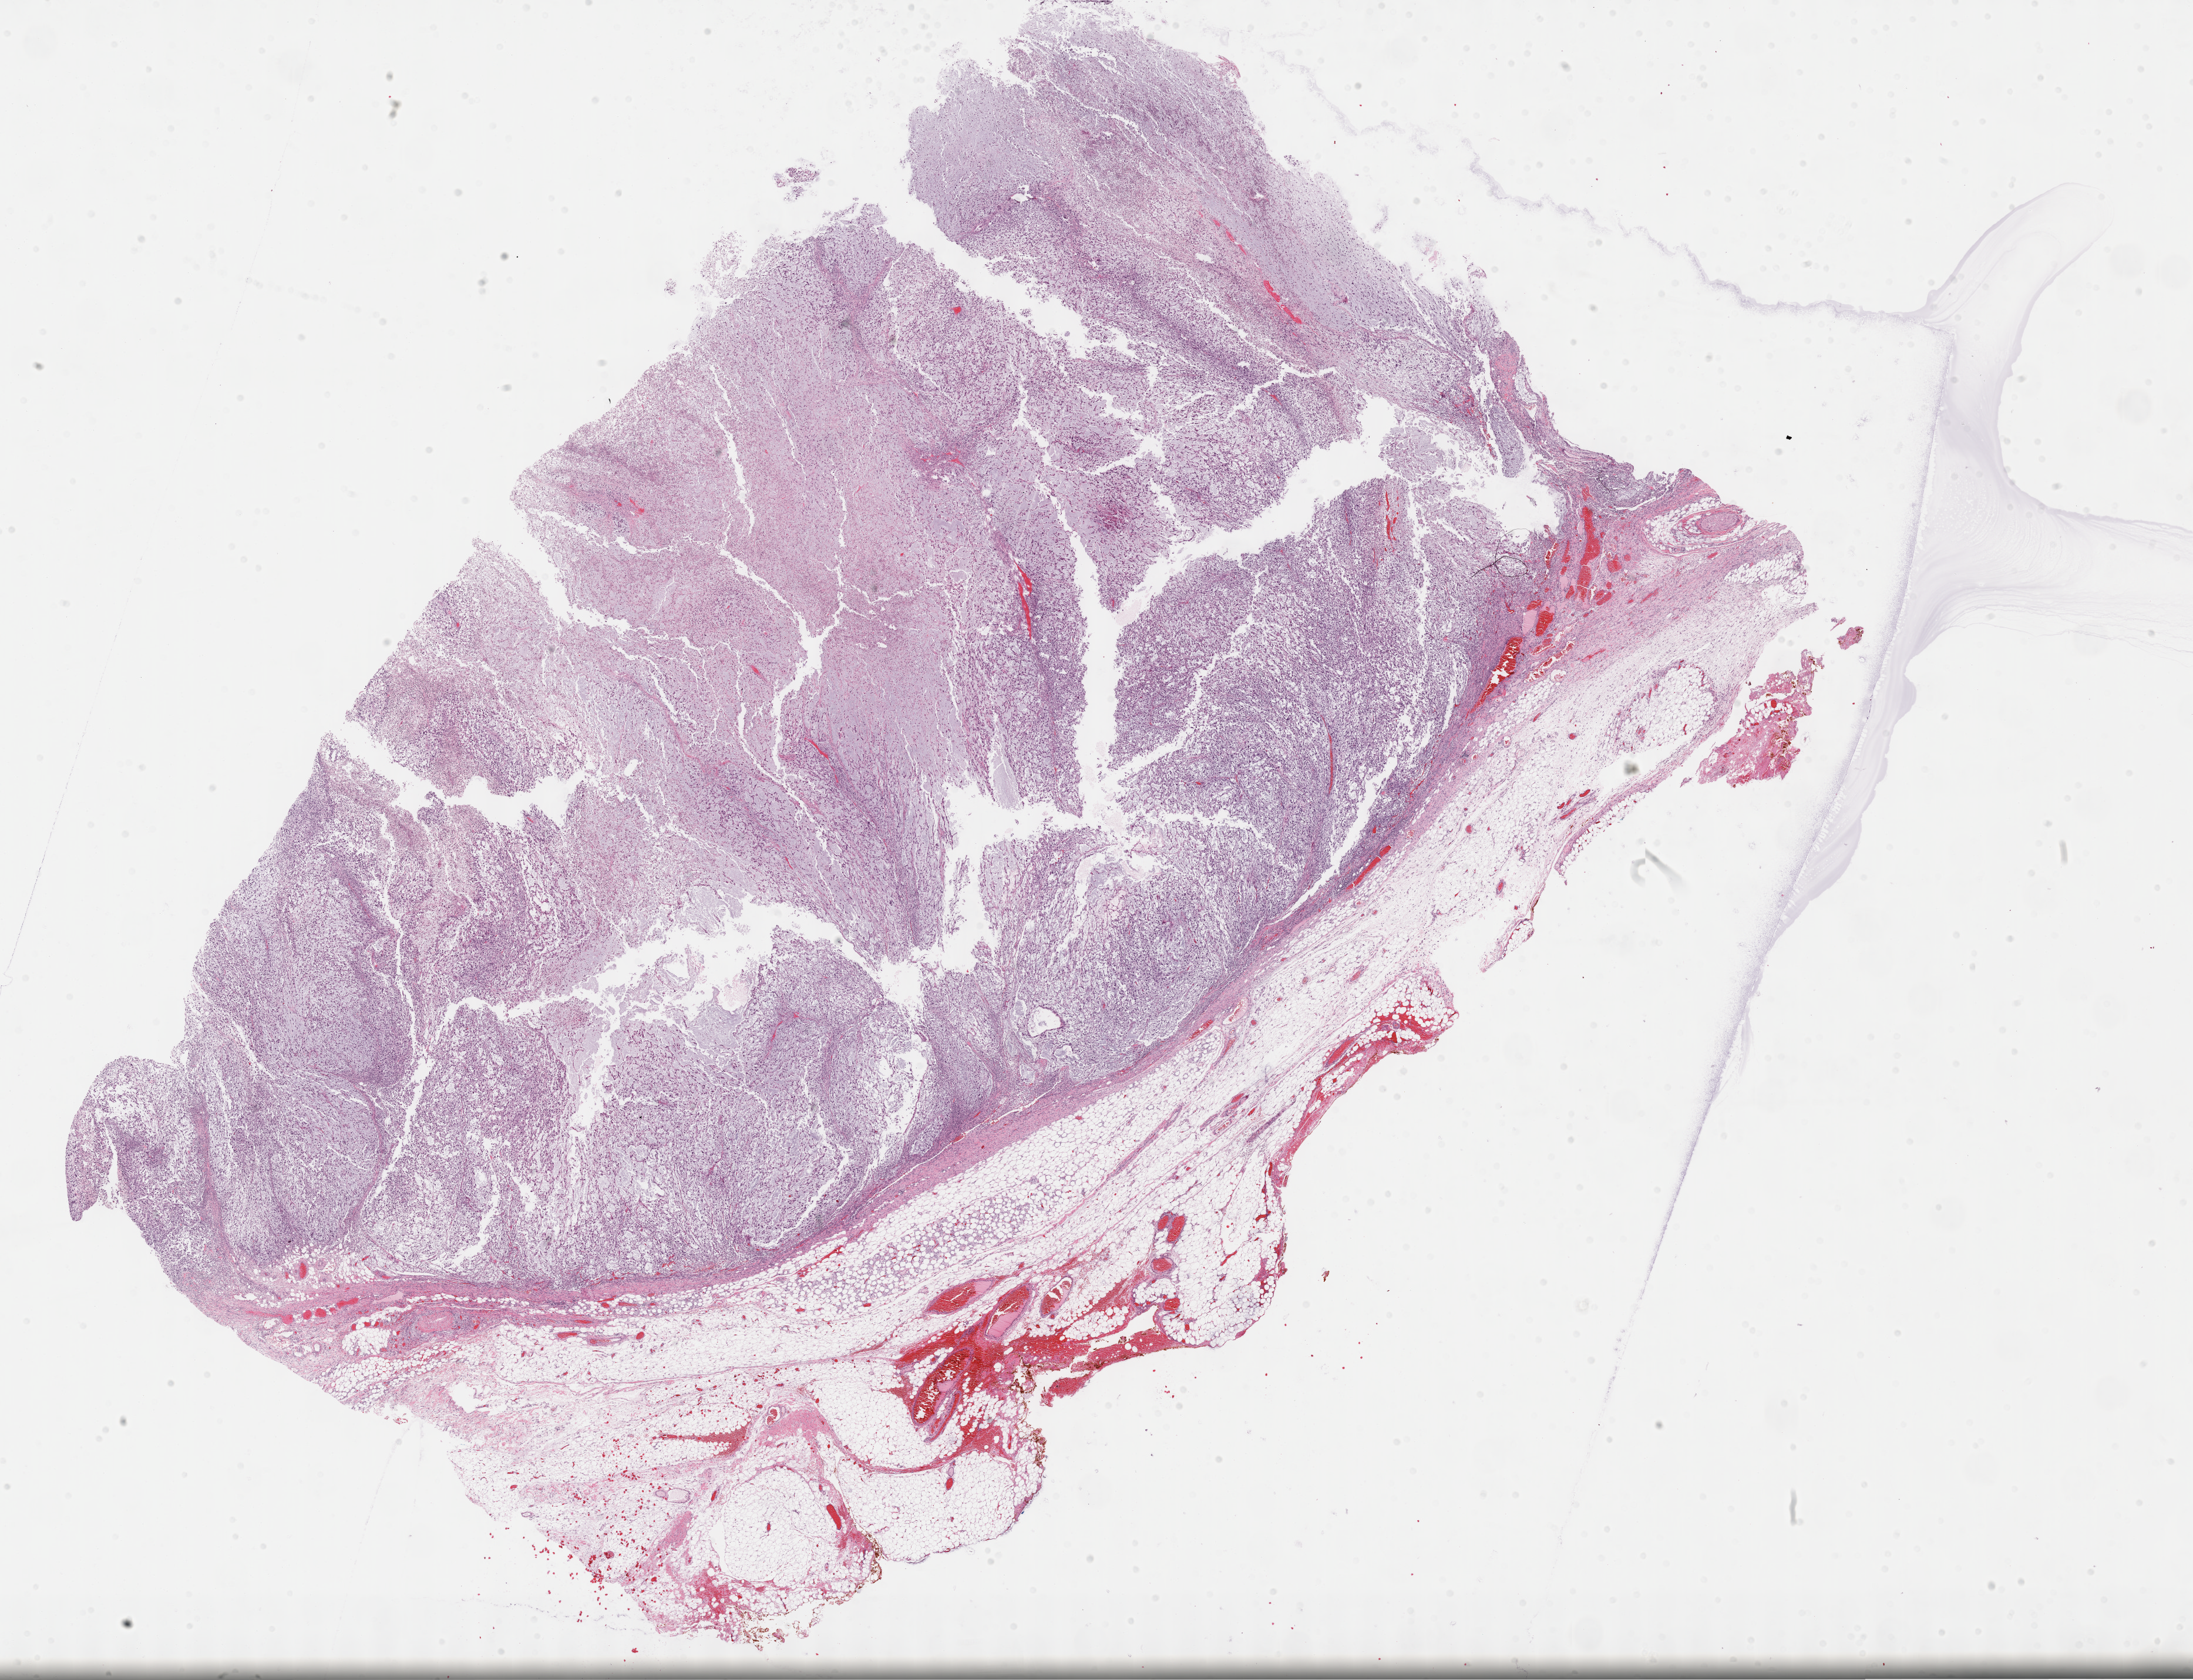
Whole-slide histology image, H&E-stained, shown as a low-resolution overview of the whole scanned area (about 30.2 x 23.1 mm, from a 40x scan). Formalin-fixed paraffin-embedded (FFPE) diagnostic section. Sample: primary tumour, connective, subcutaneous and other soft tissues. Patient: male, age at initial diagnosis 60 years.
Histologic diagnosis: Fibromyxosarcoma (connective, subcutaneous and other soft tissues of thorax).